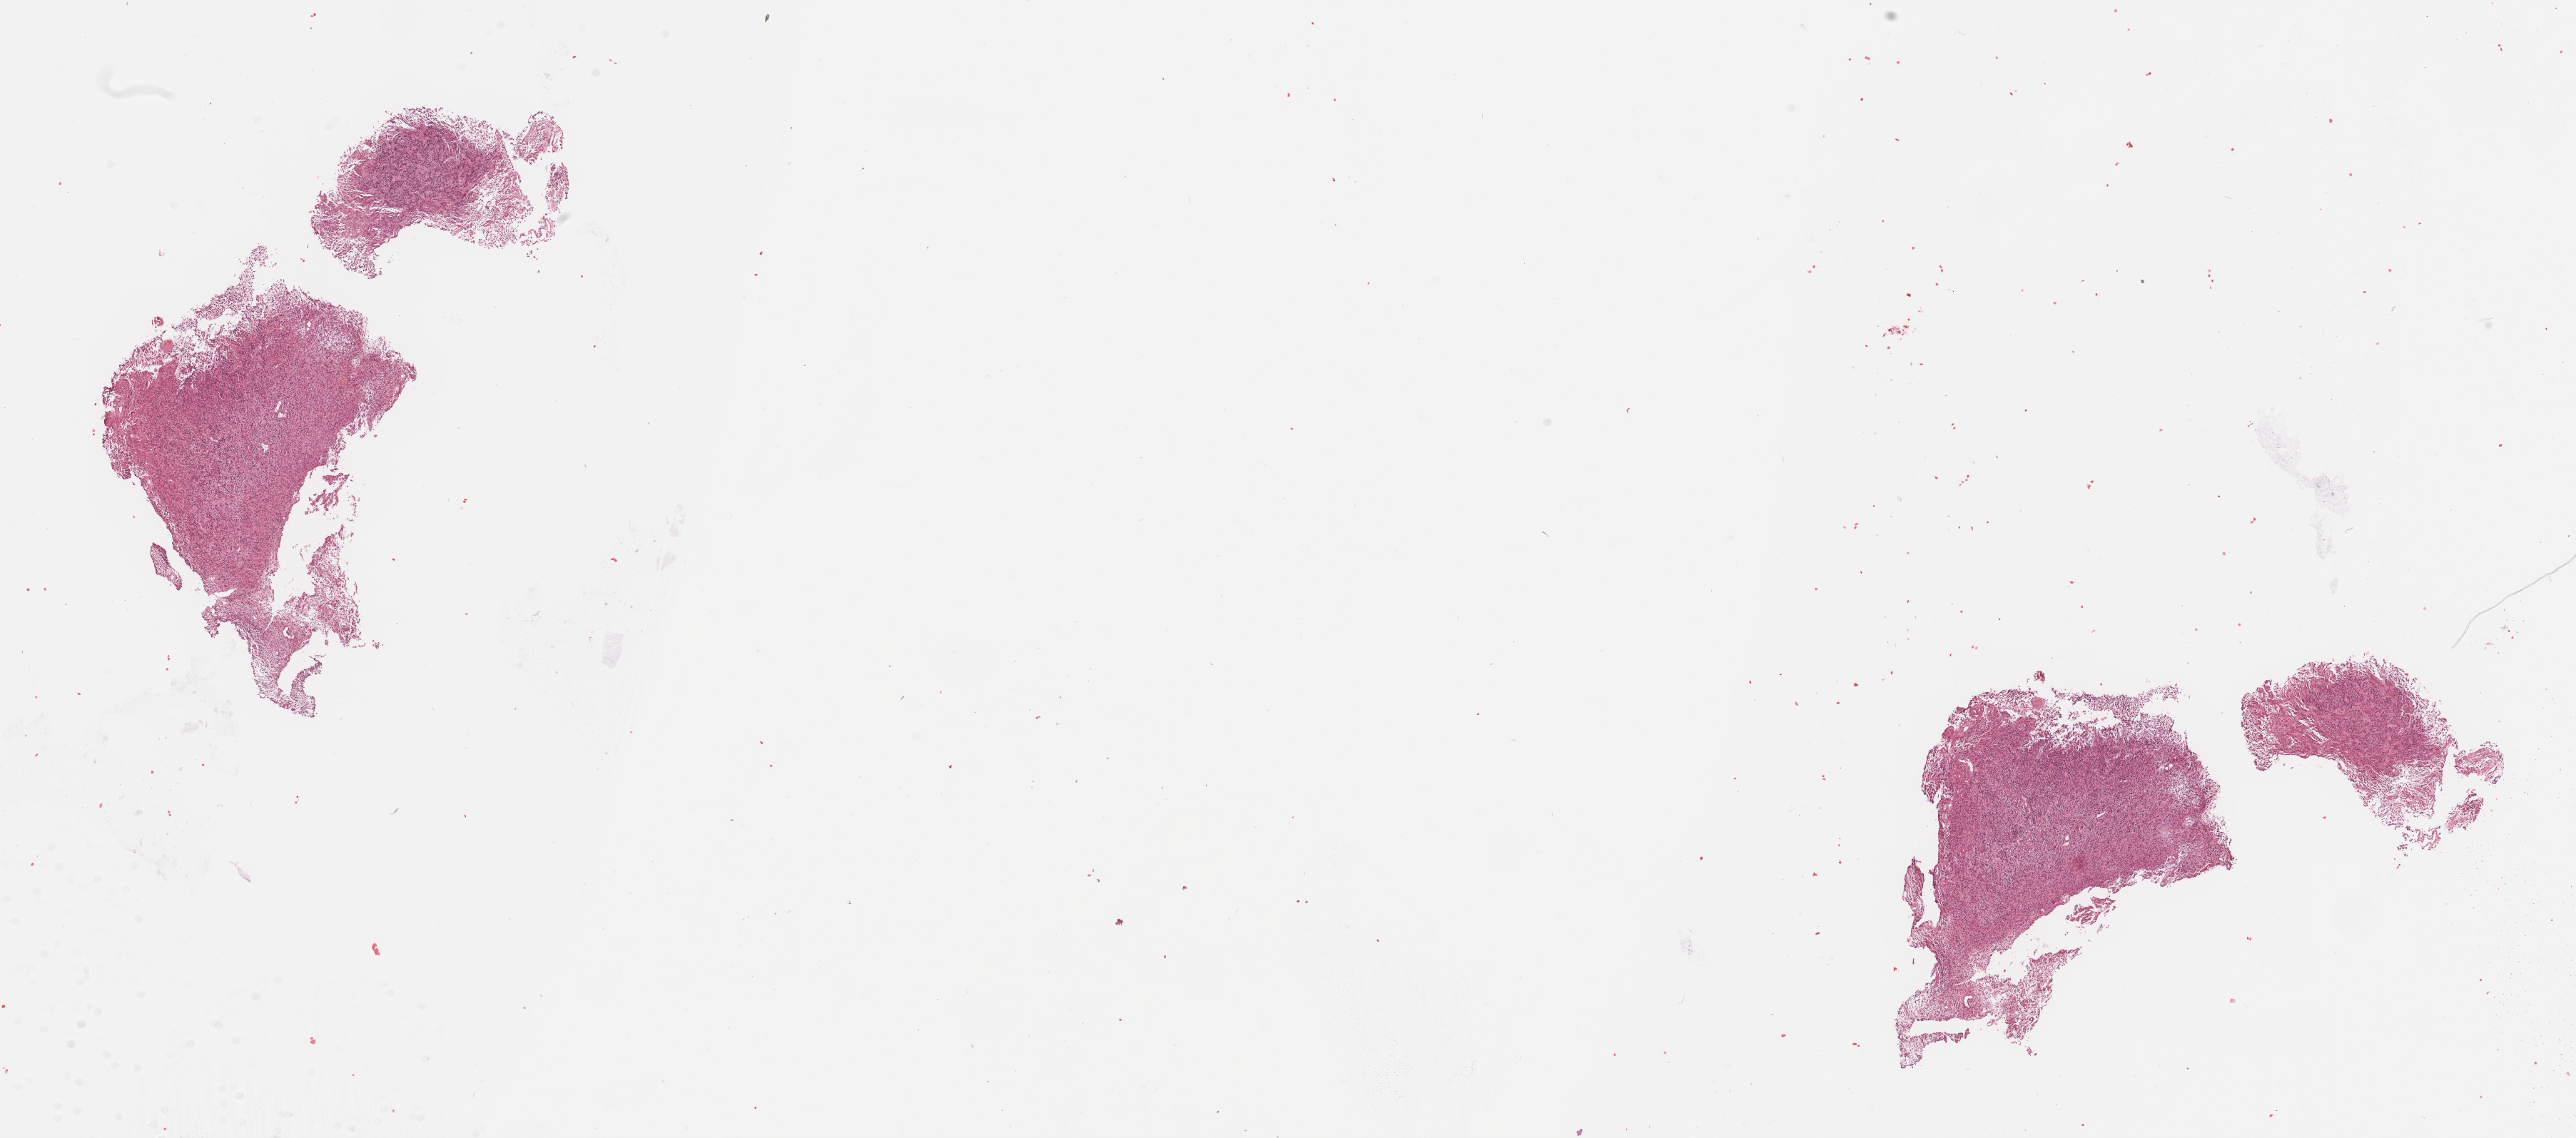
Hematoxylin and eosin (H&E) stained whole-slide image, whole scanned area (about 28.5 x 12.6 mm, slide scanned at 20x) shown as a low-resolution overview. Tumour tissue sample, sampled site: brain. 77-year-old female patient. Slide review estimates, as recorded: tumour nuclei 85%, necrosis 5%.
• primary tumour site (as recorded): temporal lobe
• histologic diagnosis: Glioblastoma